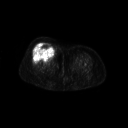
FDG PET of an extremity soft-tissue mass (from a PET/CT study), one axial slice; position 40 of 267 along the scan axis; 3.27 mm slice thickness; 128 × 128 image matrix, field of view 700 × 700 mm. Female patient, age 56 years. Case-level facts recorded for this patient, not image findings: histological type: malignant solitary fibrous tumor; grade: intermediate; site of the primary tumour: right thigh.
Annotated regions visible in this slice (expert contour drawn on MRI and transferred to this co-registered scan by the dataset authors):
- gross tumour volume including surrounding oedema: bounding box (x1, y1, x2, y2) in pixels: (32, 42, 56, 60)
- gross tumour volume (mass): (33, 42, 55, 60)